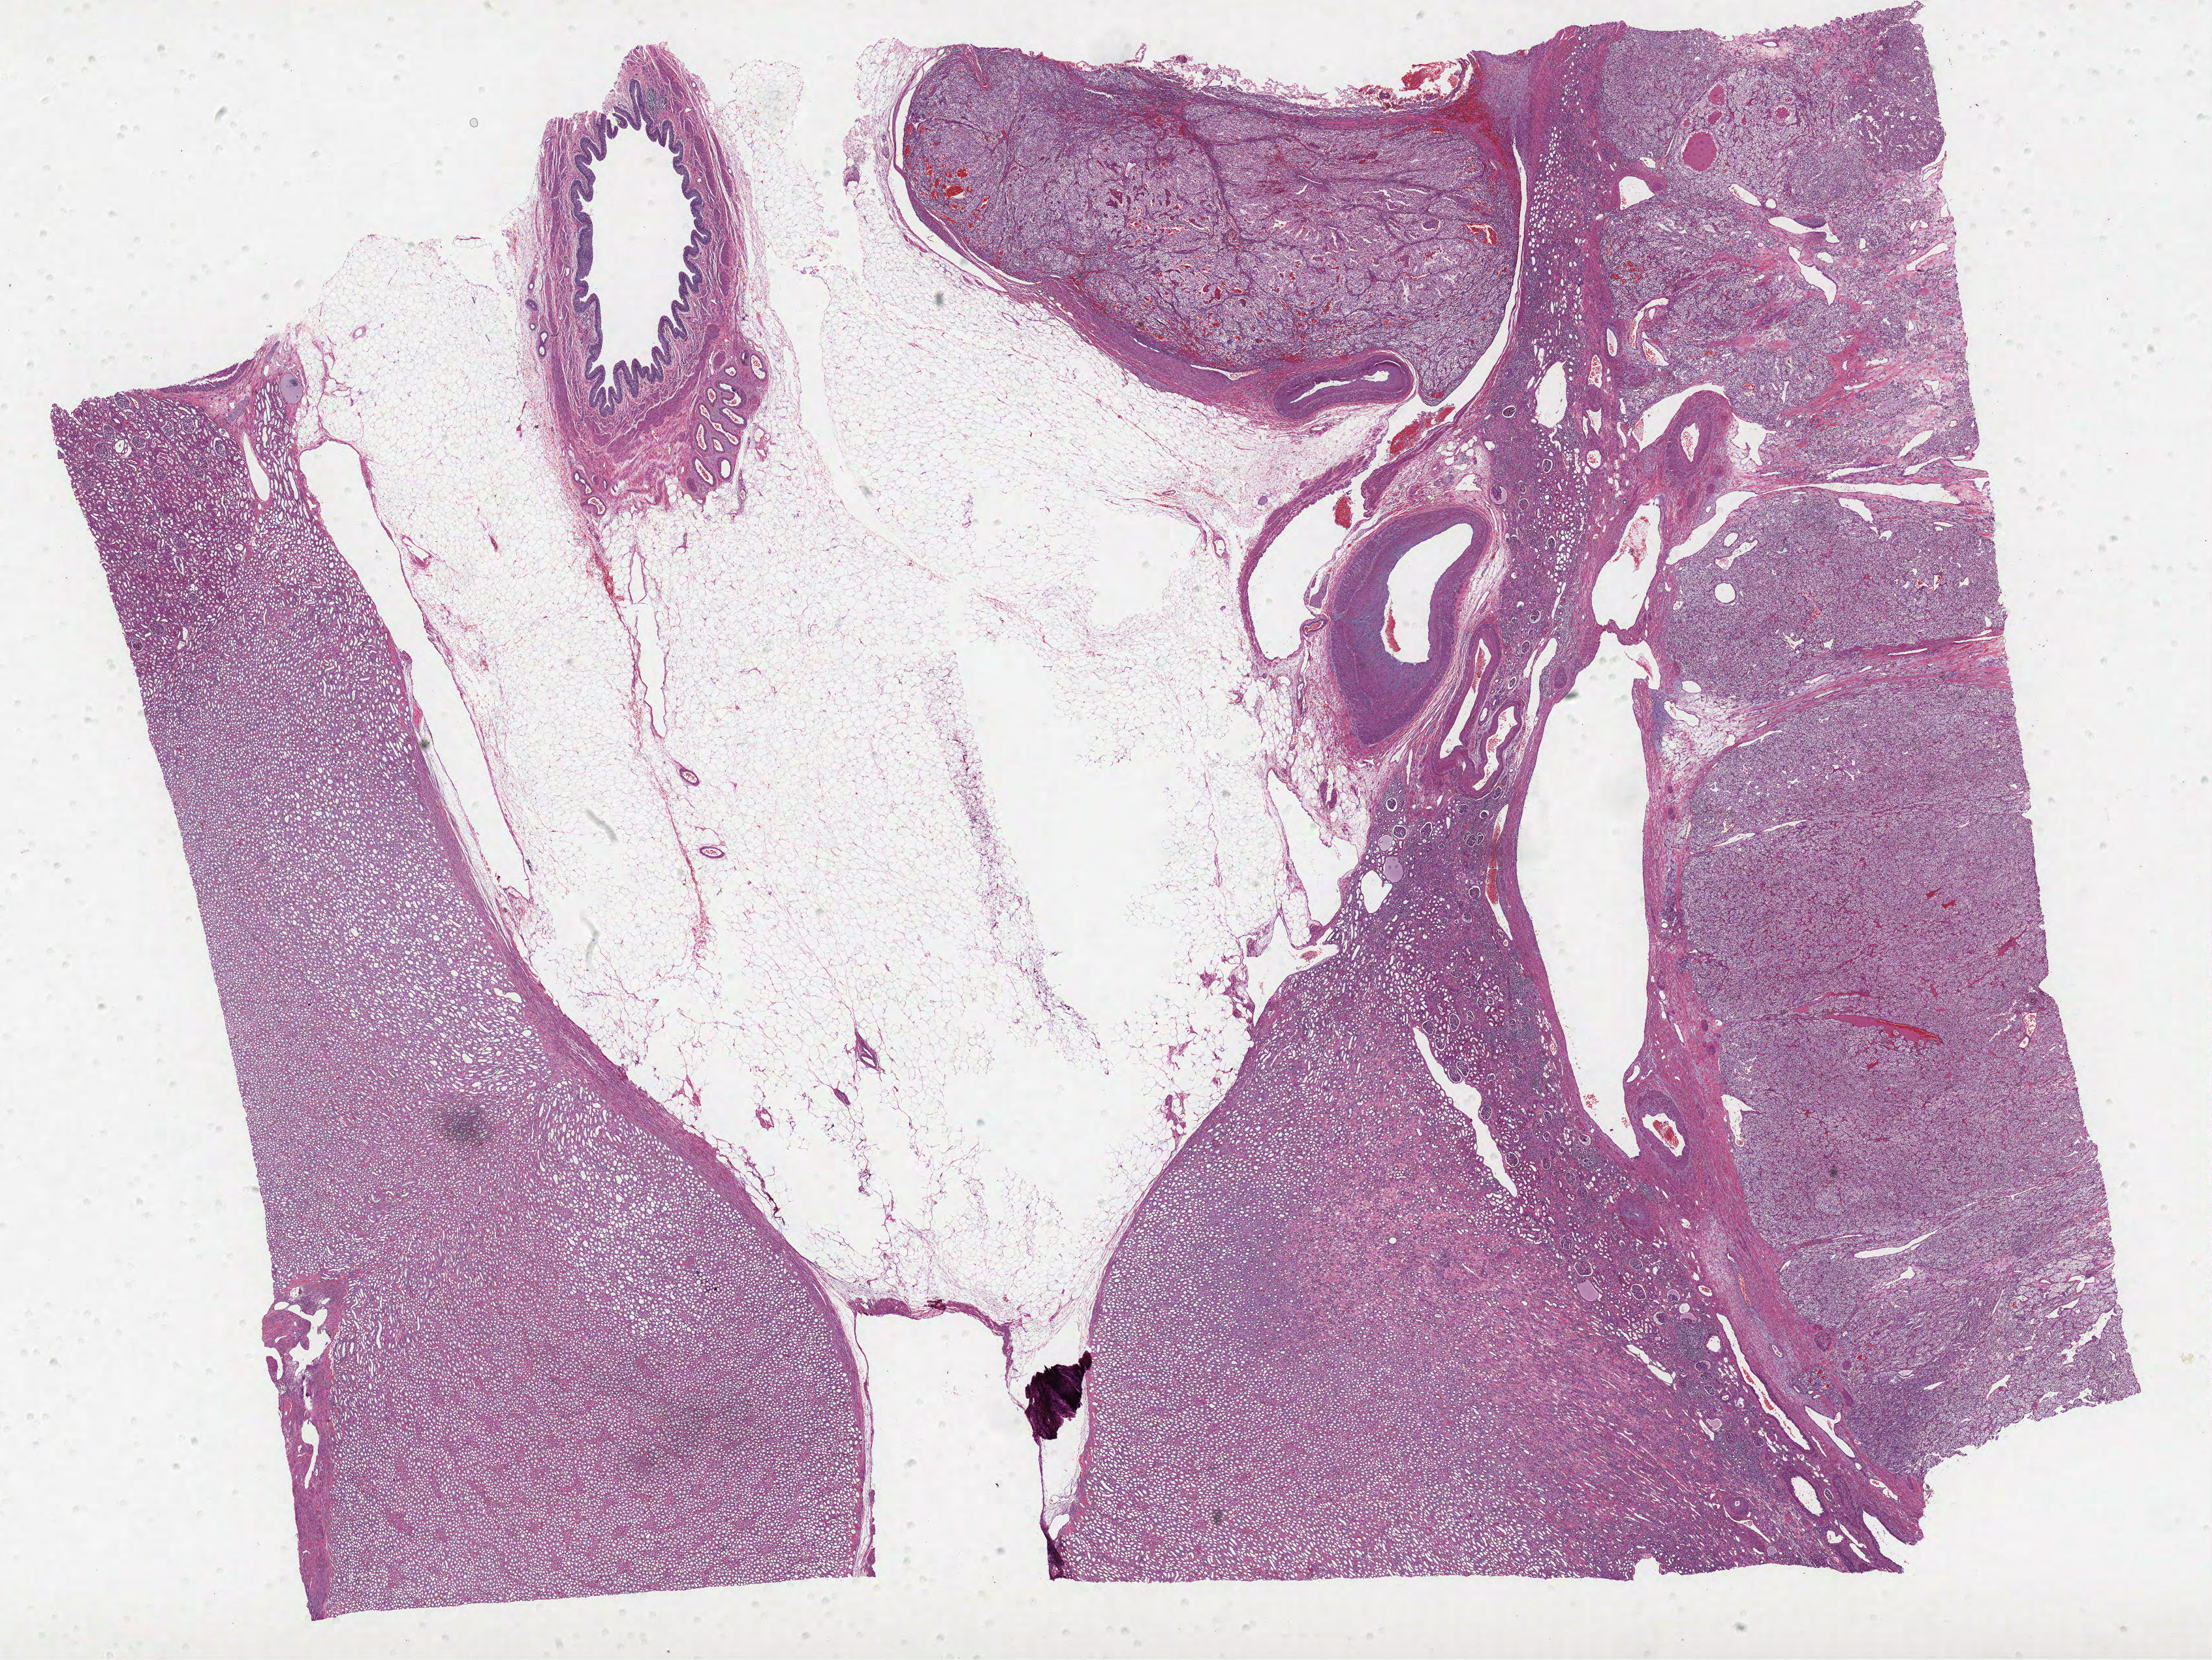
Digitized H&E-stained tissue section (whole slide) — a low-resolution overview of the entire scanned area, about 27.1 x 20.3 mm; formalin-fixed paraffin-embedded (FFPE) diagnostic section; primary tumour sample from the kidney. Male patient; age at initial diagnosis 58 years. Histologic grade: G3 (poorly differentiated).
Laterality: right. Histologic diagnosis: Clear cell adenocarcinoma, NOS. Lymph nodes positive (case pathology): 0 of 10 examined. AJCC pathologic stage: III.